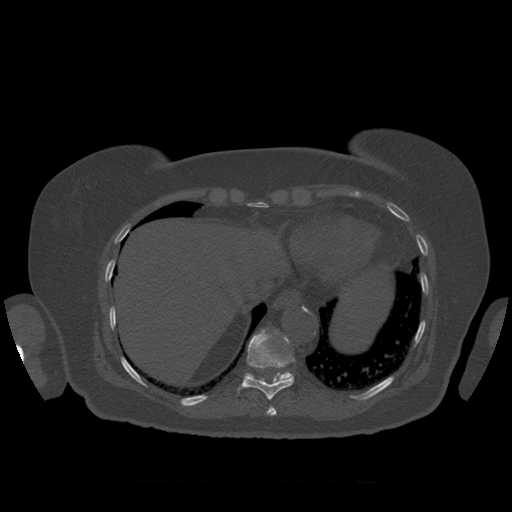
CT including the spine, one axial slice. Slice 337 of 399 in the series (ordered by position). Reconstruction kernel STANDARD. 120 kVp. Bone window (W 1800 / L 400 HU). 1.25 mm slice thickness. 512 × 512 image matrix. Patient age 81 years. From the clinical record (not read from this slice): primary cancer: renal; vertebrae with lytic lesions (as recorded): L1.
Structures marked on this image (semi-automatically segmented with operator editing):
- T10 vertebra: bounding box <238,330,295,400> (left, top, right, bottom; pixels)
- T11 vertebra: <246,332,293,381>
- T9 vertebra: <267,406,277,416>